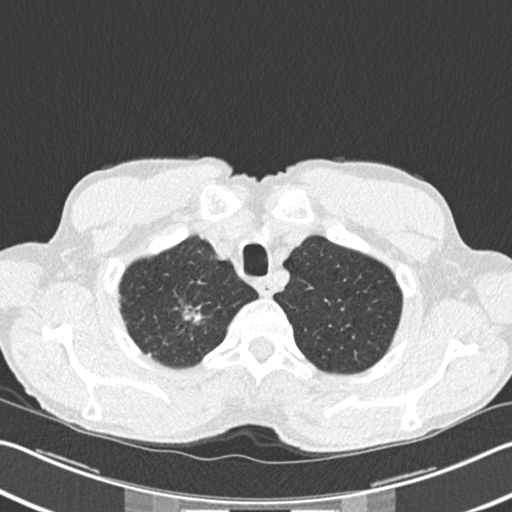
Axial slice from a low-dose chest CT screening exam; second annual screen; lung window (W 1500 / L -600 HU); standard (soft-tissue) reconstruction kernel (B30f). Male participant, aged 62 years at enrolment. Former smoker at enrolment.
• Expert reader's lesion annotation, bounding box (x1, y1, x2, y2) in pixels: (167, 297, 210, 342).
• The screening reader recorded 2 non-calcified nodules or masses ≥4 mm on this exam (right upper lobe, right upper lobe); which of them this box marks is not recorded.
• Lung cancer was diagnosed 5 days after this screen: bronchiolo-alveolar adenocarcinoma, NOS, right upper lobe, well differentiated (G1), stage IA (AJCC 6th edition), 15 mm at pathology.